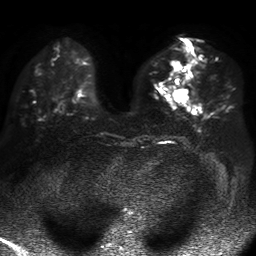
Breast MRI, one axial slice; position 21 of 50 along the scan axis; diffusion-weighted series; image 2 of 4 stored at this slice position (different b-values; order by instance number); 1.5 T; 4 mm slice thickness; 256 × 256 image matrix, field of view 360 × 360 mm. Female patient.
Outlined on this slice (expert manual segmentation):
- tumour on diffusion-weighted imaging: bounding box [x1, y1, x2, y2] px = [170, 60, 188, 102]